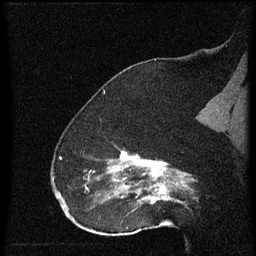
Breast MRI (dynamic contrast-enhanced), one sagittal slice. Slice 41 of 60 in the series (ordered by position). Dynamic contrast-enhanced series, image 2 of 4 at this slice position (ordered by acquisition). 1.5 T. TE 4.2 ms, TR 8 ms. 2 mm slice thickness. 256 × 256 image matrix, field of view 180 × 180 mm. Patient: female, 52 years.
Structures marked on this image (semi-automatically segmented with operator editing):
- analysis volume of interest (the breast-tissue region the enhancement analysis was run in; not a lesion): box from (x=73, y=150) to (x=172, y=219) px
- tumour enhancement mask (voxels above the 70 % enhancement threshold inside the analysis volume of interest): (x=86, y=152)–(x=172, y=203)